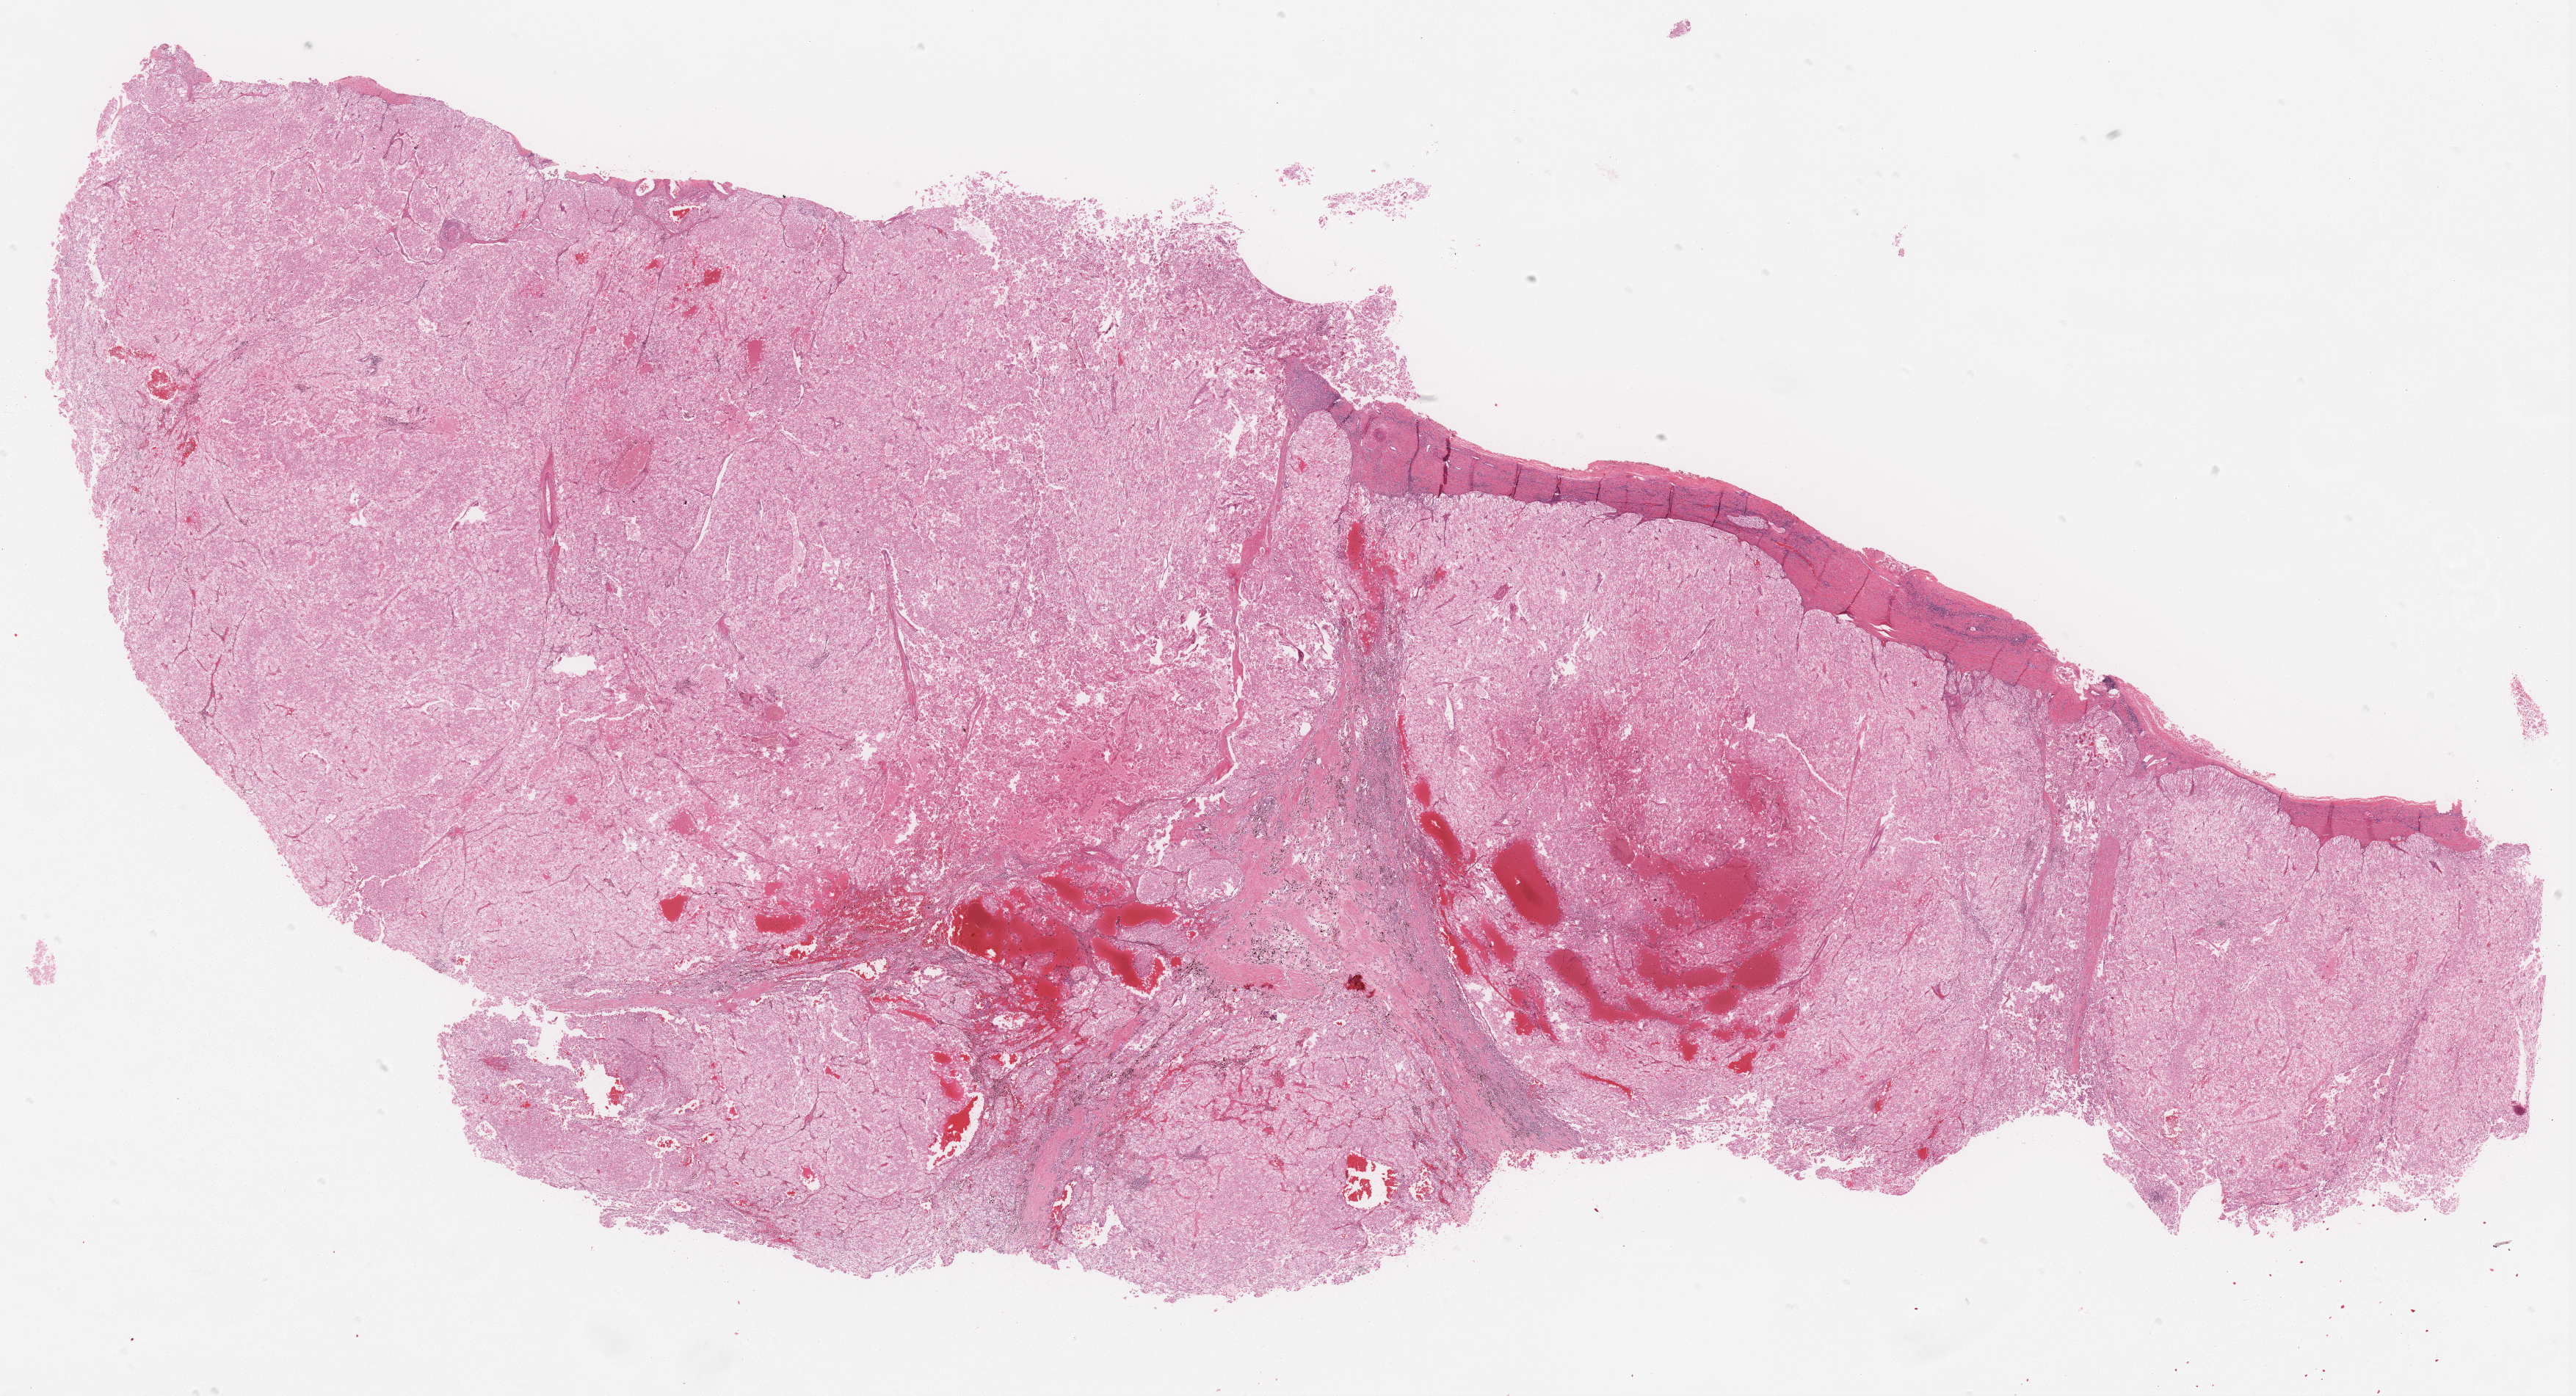
Whole-slide histology image, H&E-stained — shown as a low-resolution overview of the whole scanned area (about 28.1 x 15.2 mm, from a 40x scan), FFPE section, sample: primary tumour, kidney. Patient: female, age at initial diagnosis 57 years.
AJCC pathologic stage: I (6th edition). TNM: T1b N0 M0. Histologic diagnosis: Renal cell carcinoma, chromophobe type. Lymph nodes positive (case pathology): 0 of 1 examined.